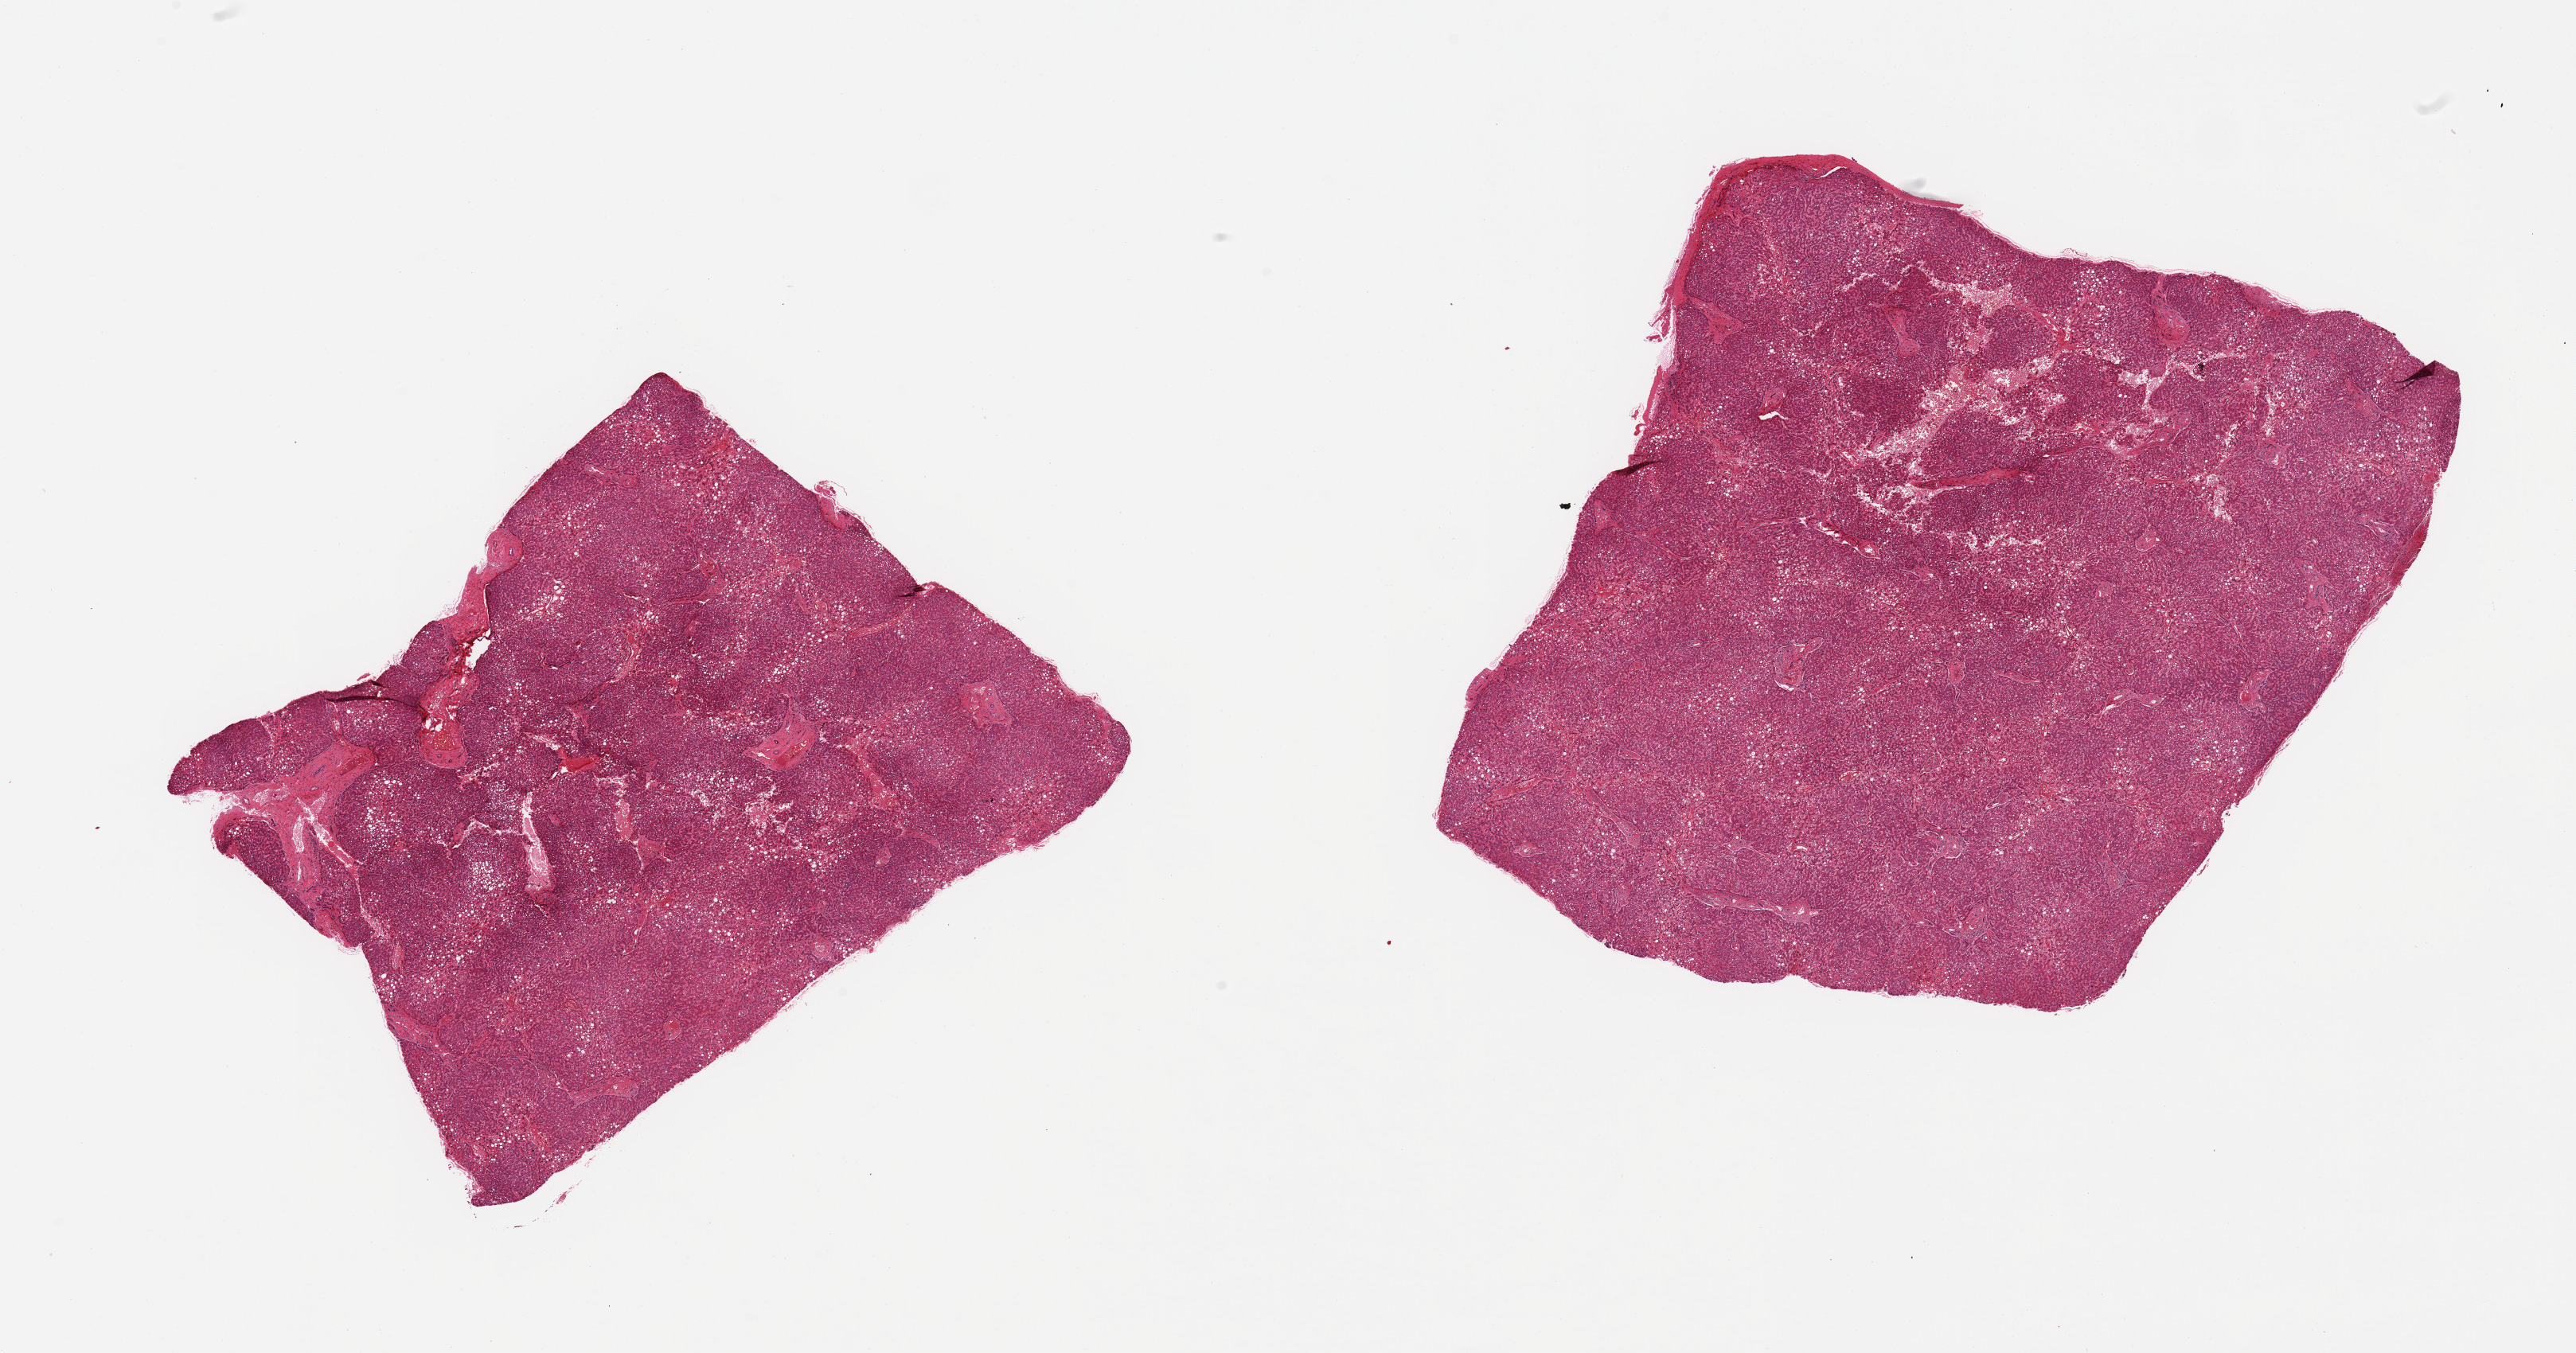
Digitized haematoxylin and eosin-stained section, brightfield — a low-resolution overview of the entire scanned area, about 25.6 x 13.4 mm (slide scanned at 20x), PAXgene-fixed, paraffin-embedded tissue, sampled site (target tissue): liver, donor tissue sample. Donor sex: male.
Pathologist's review note for this sample: 2 pieces, macro and microvesicular steatosis involves ~50% of parenchyma. Mild passive congestion.